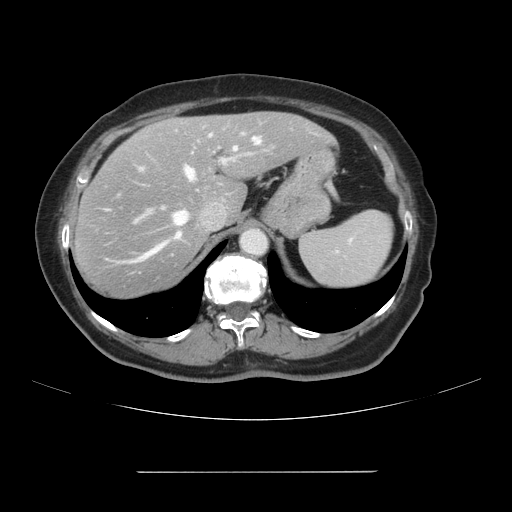
Contrast-enhanced abdominal CT, one axial slice; slice 77 of 111 in the series (ordered by position); 120 kVp; intravenous contrast given; soft-tissue window (W 400 / L 40 HU); 2.5 mm slice thickness; 512 × 512 image matrix, field of view 400 × 400 mm. Female patient, age 74 years. From the clinical record (not read from this slice): diagnosis: colorectal cancer liver metastases, imaged before liver resection.
Outlined on this slice (expert manual segmentation):
- hepatic veins: box from (x=105, y=137) to (x=261, y=265) px
- liver: (x=72, y=112)–(x=333, y=299)
- planned liver remnant (the part of the liver to remain after resection): (x=157, y=112)–(x=332, y=220)
- portal vein (with intrahepatic branches): (x=140, y=134)–(x=244, y=171)